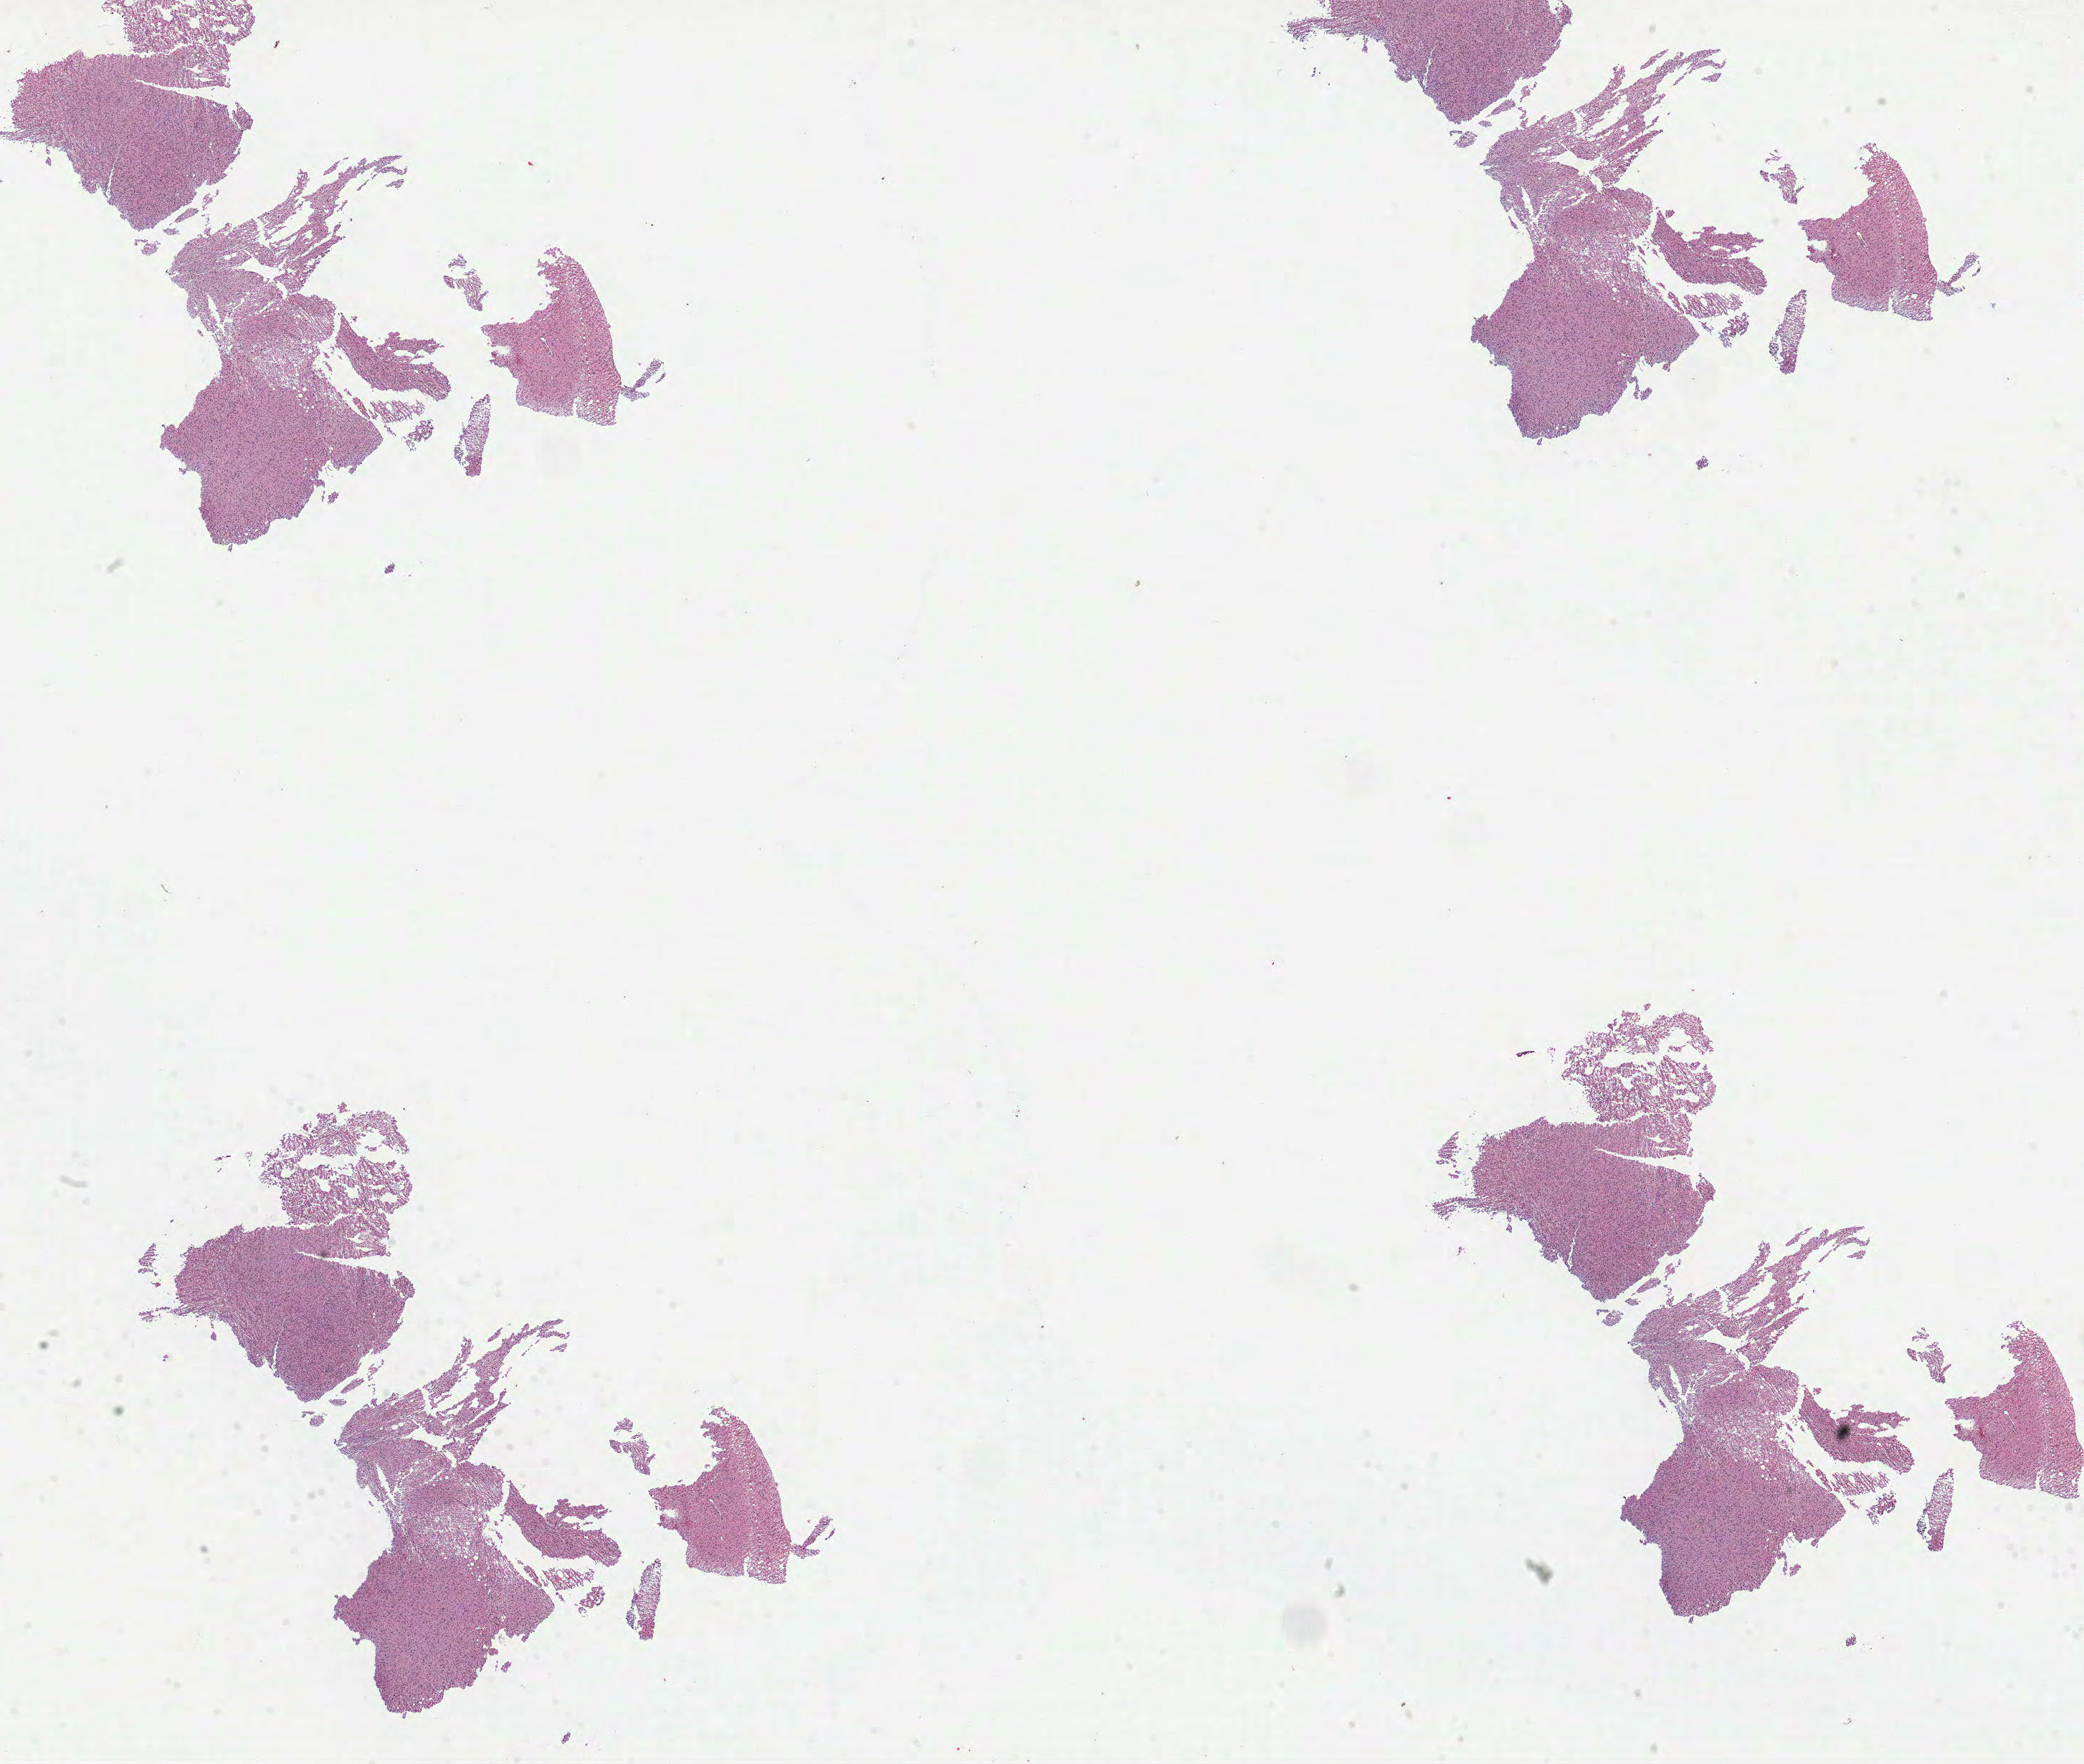
H&E whole-slide image — a low-resolution overview of the entire scanned area, about 23.4 x 19.9 mm (from a 40x scan). Formalin-fixed paraffin-embedded (FFPE) diagnostic section. Brain, primary tumour sample. Patient: female, age at initial diagnosis 60 years.
Diagnosis: Mixed glioma.